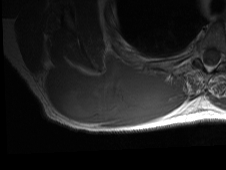
MRI of an extremity soft-tissue mass, one axial slice; position 29 of 81 along the scan axis; MR volume resampled by the dataset authors to the PET/CT grid (not the native acquisition matrix); 3.27 mm slice thickness; 226 × 170 image matrix, field of view 221 × 166 mm. Male patient. Case-level facts recorded for this patient, not image findings: histological type: pleiomorphic spindle cell undifferentiated; grade: high; site of the primary tumour: right parascapusular.
Annotated regions visible in this slice (expert contour drawn on MRI and transferred to this co-registered scan by the dataset authors):
- gross tumour volume including surrounding oedema: box from (x=44, y=56) to (x=186, y=126) px
- gross tumour volume (mass): (x=44, y=56)–(x=168, y=123)